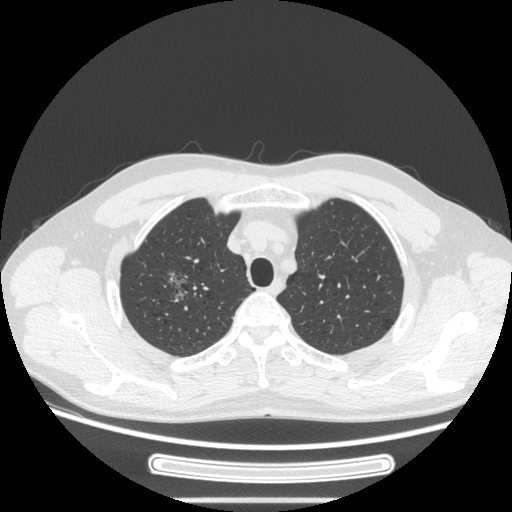
Chest CT, one axial slice. Slice 217 of 269 in the series (ordered by position). 120 kVp. Lung window (W 1500 / L -600 HU). 1.25 mm slice thickness. 512 × 512 image matrix, field of view 382 × 382 mm. Male patient, age 53 years. Case-level facts recorded for this patient, not image findings: clinical TNM (as recorded): T1c N0 M0; histopathological grade: G2.
Annotated regions visible in this slice (bounding box drawn by a radiologist):
- lung tumour (recorded histology: adenocarcinoma): bounding box (x1, y1, x2, y2) in pixels: (160, 263, 196, 310)